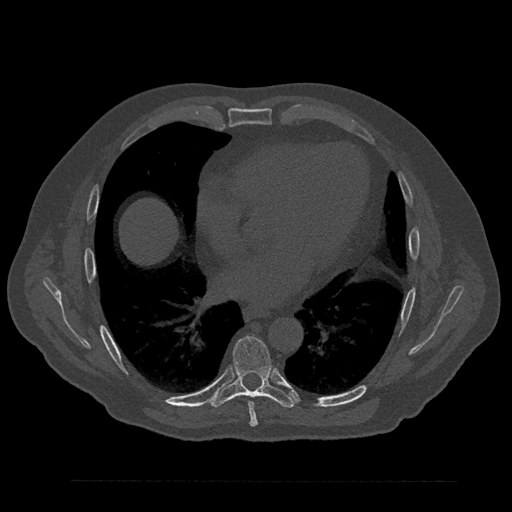
CT including the spine, one axial slice; position 469 of 797 along the scan axis; bone window (W 1800 / L 400 HU); 512 × 512 image matrix, field of view 430 × 430 mm. Male patient, age 61 years. From the clinical record (not read from this slice): primary cancer: prostate.
Annotated regions visible in this slice (semi-automatically segmented with operator editing):
- T7 vertebra: bounding box <248,402,258,427> (left, top, right, bottom; pixels)
- T8 vertebra: <211,336,296,408>